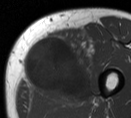
MRI of an extremity soft-tissue mass, one axial slice. Position 22 of 55 along the scan axis. MR volume resampled by the dataset authors to the PET/CT grid (not the native acquisition matrix). 3.27 mm slice thickness. 131 × 118 image matrix. Male patient. From the clinical record (not read from this slice): histological type: pleiomorphic liposarcoma; grade: high; site of the primary tumour: left thigh.
Outlined on this slice (expert contour drawn on MRI and transferred to this co-registered scan by the dataset authors):
- gross tumour volume including surrounding oedema: bounding box [x1, y1, x2, y2] px = [23, 30, 99, 104]
- gross tumour volume (mass): [23, 34, 90, 97]